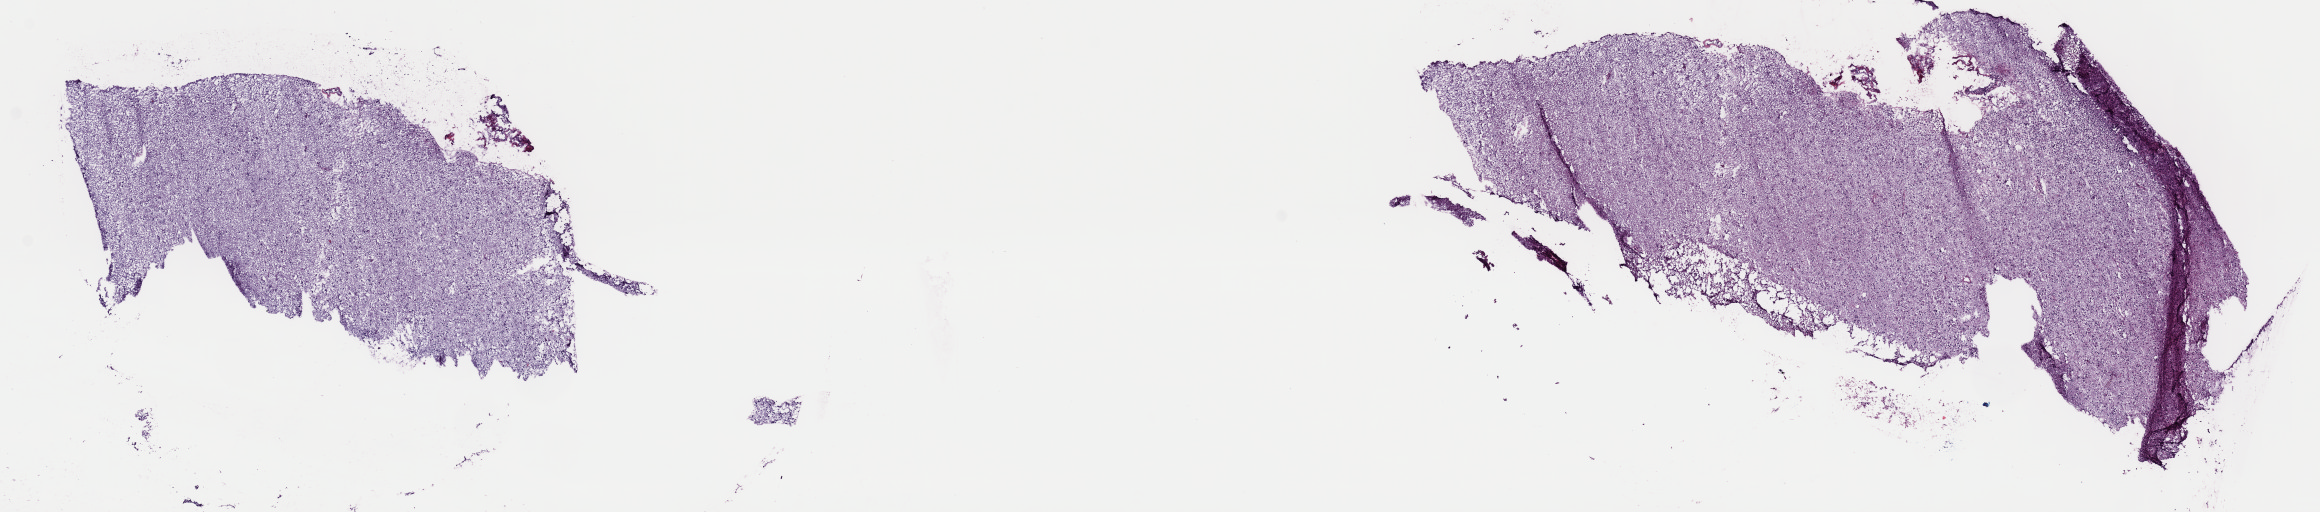
Whole-slide histology image, Hematoxylin and eosin (H&E) stained, shown as a low-resolution overview of the whole scanned area (about 18.3 x 4.0 mm, slide scanned at 40x); frozen section from the top of the tissue portion; primary tumour sample from the brain. Patient: female, age at initial diagnosis 50 years. Histologic grade: G2 (moderately differentiated). Pathologist review of this section (percent, as recorded): tumour cells 50%, tumour nuclei 70%, normal cells 10%, stromal cells 40%, necrosis 0%. Infiltration values recorded for this section: lymphocyte infiltration 0%, monocyte infiltration 0%, neutrophil infiltration 0%.
Pathologic diagnosis: Oligodendroglioma, NOS (cerebrum). Laterality: left.